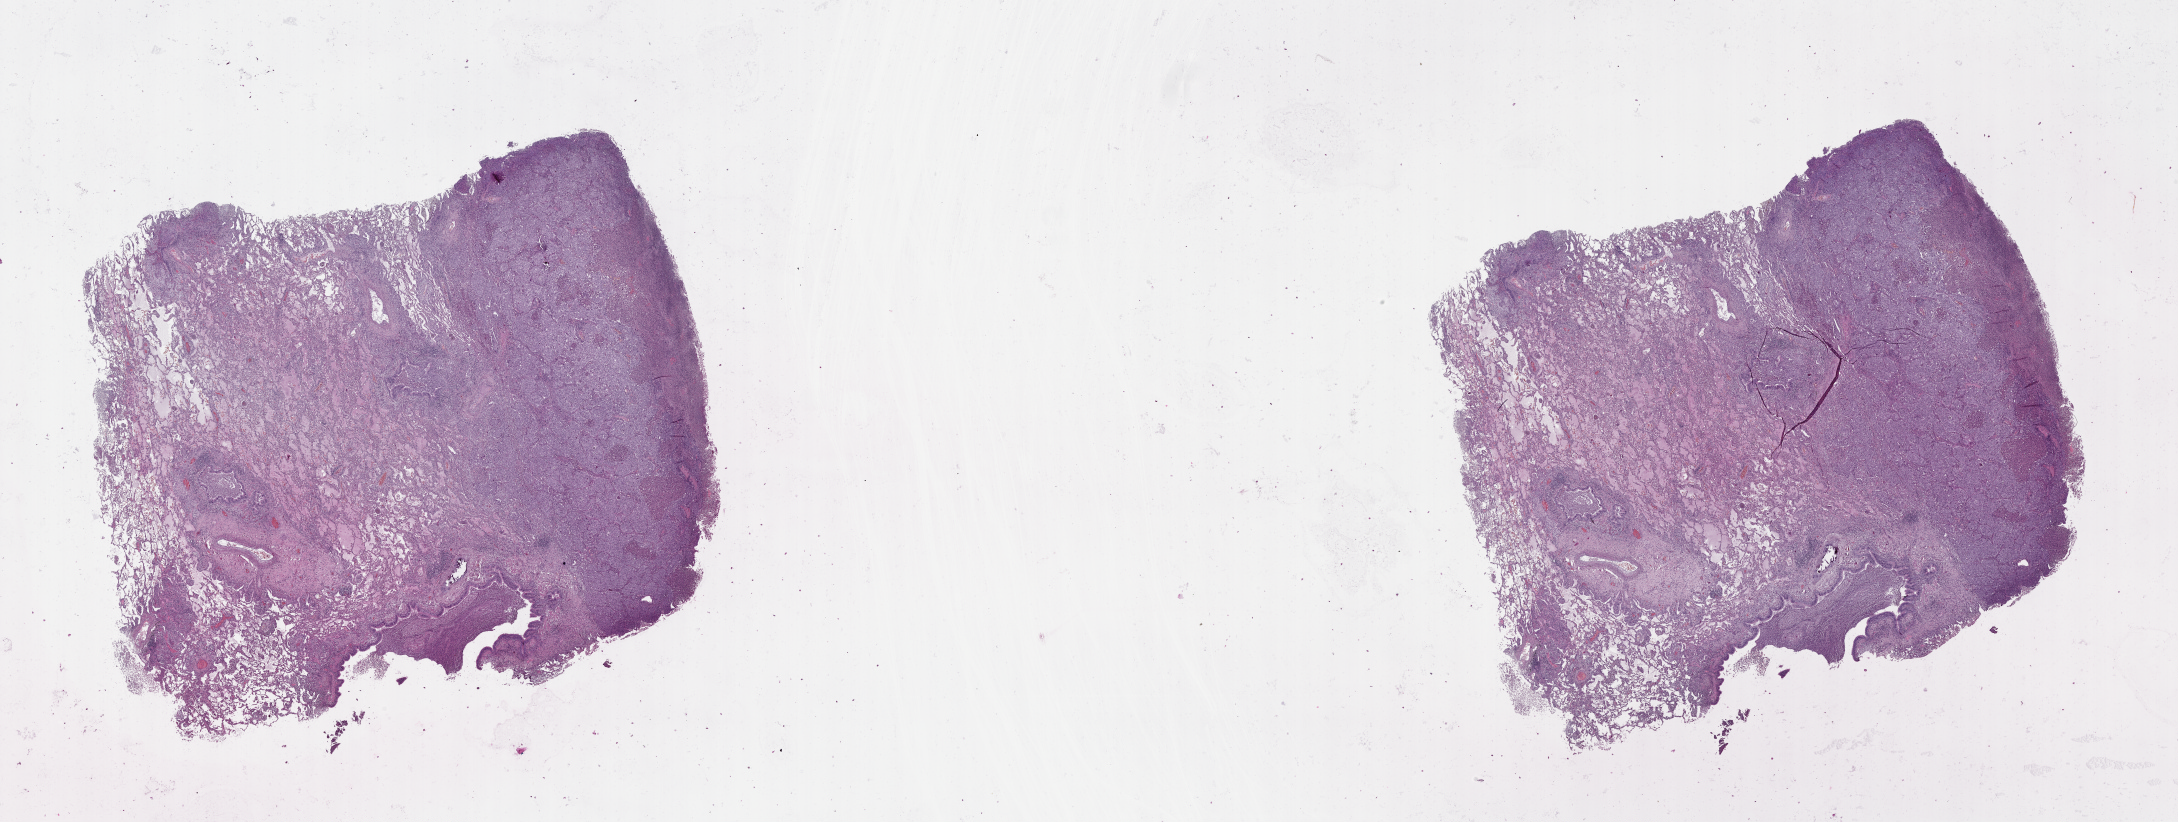
Digitized H&E-stained tissue section (whole slide), shown as a low-resolution overview of the whole scanned area (about 35.1 x 13.2 mm, acquisition: 20x scan), lung, tumour tissue. 67-year-old male patient.
- patient diagnosis (cohort enrolment): squamous cell carcinoma (lung)